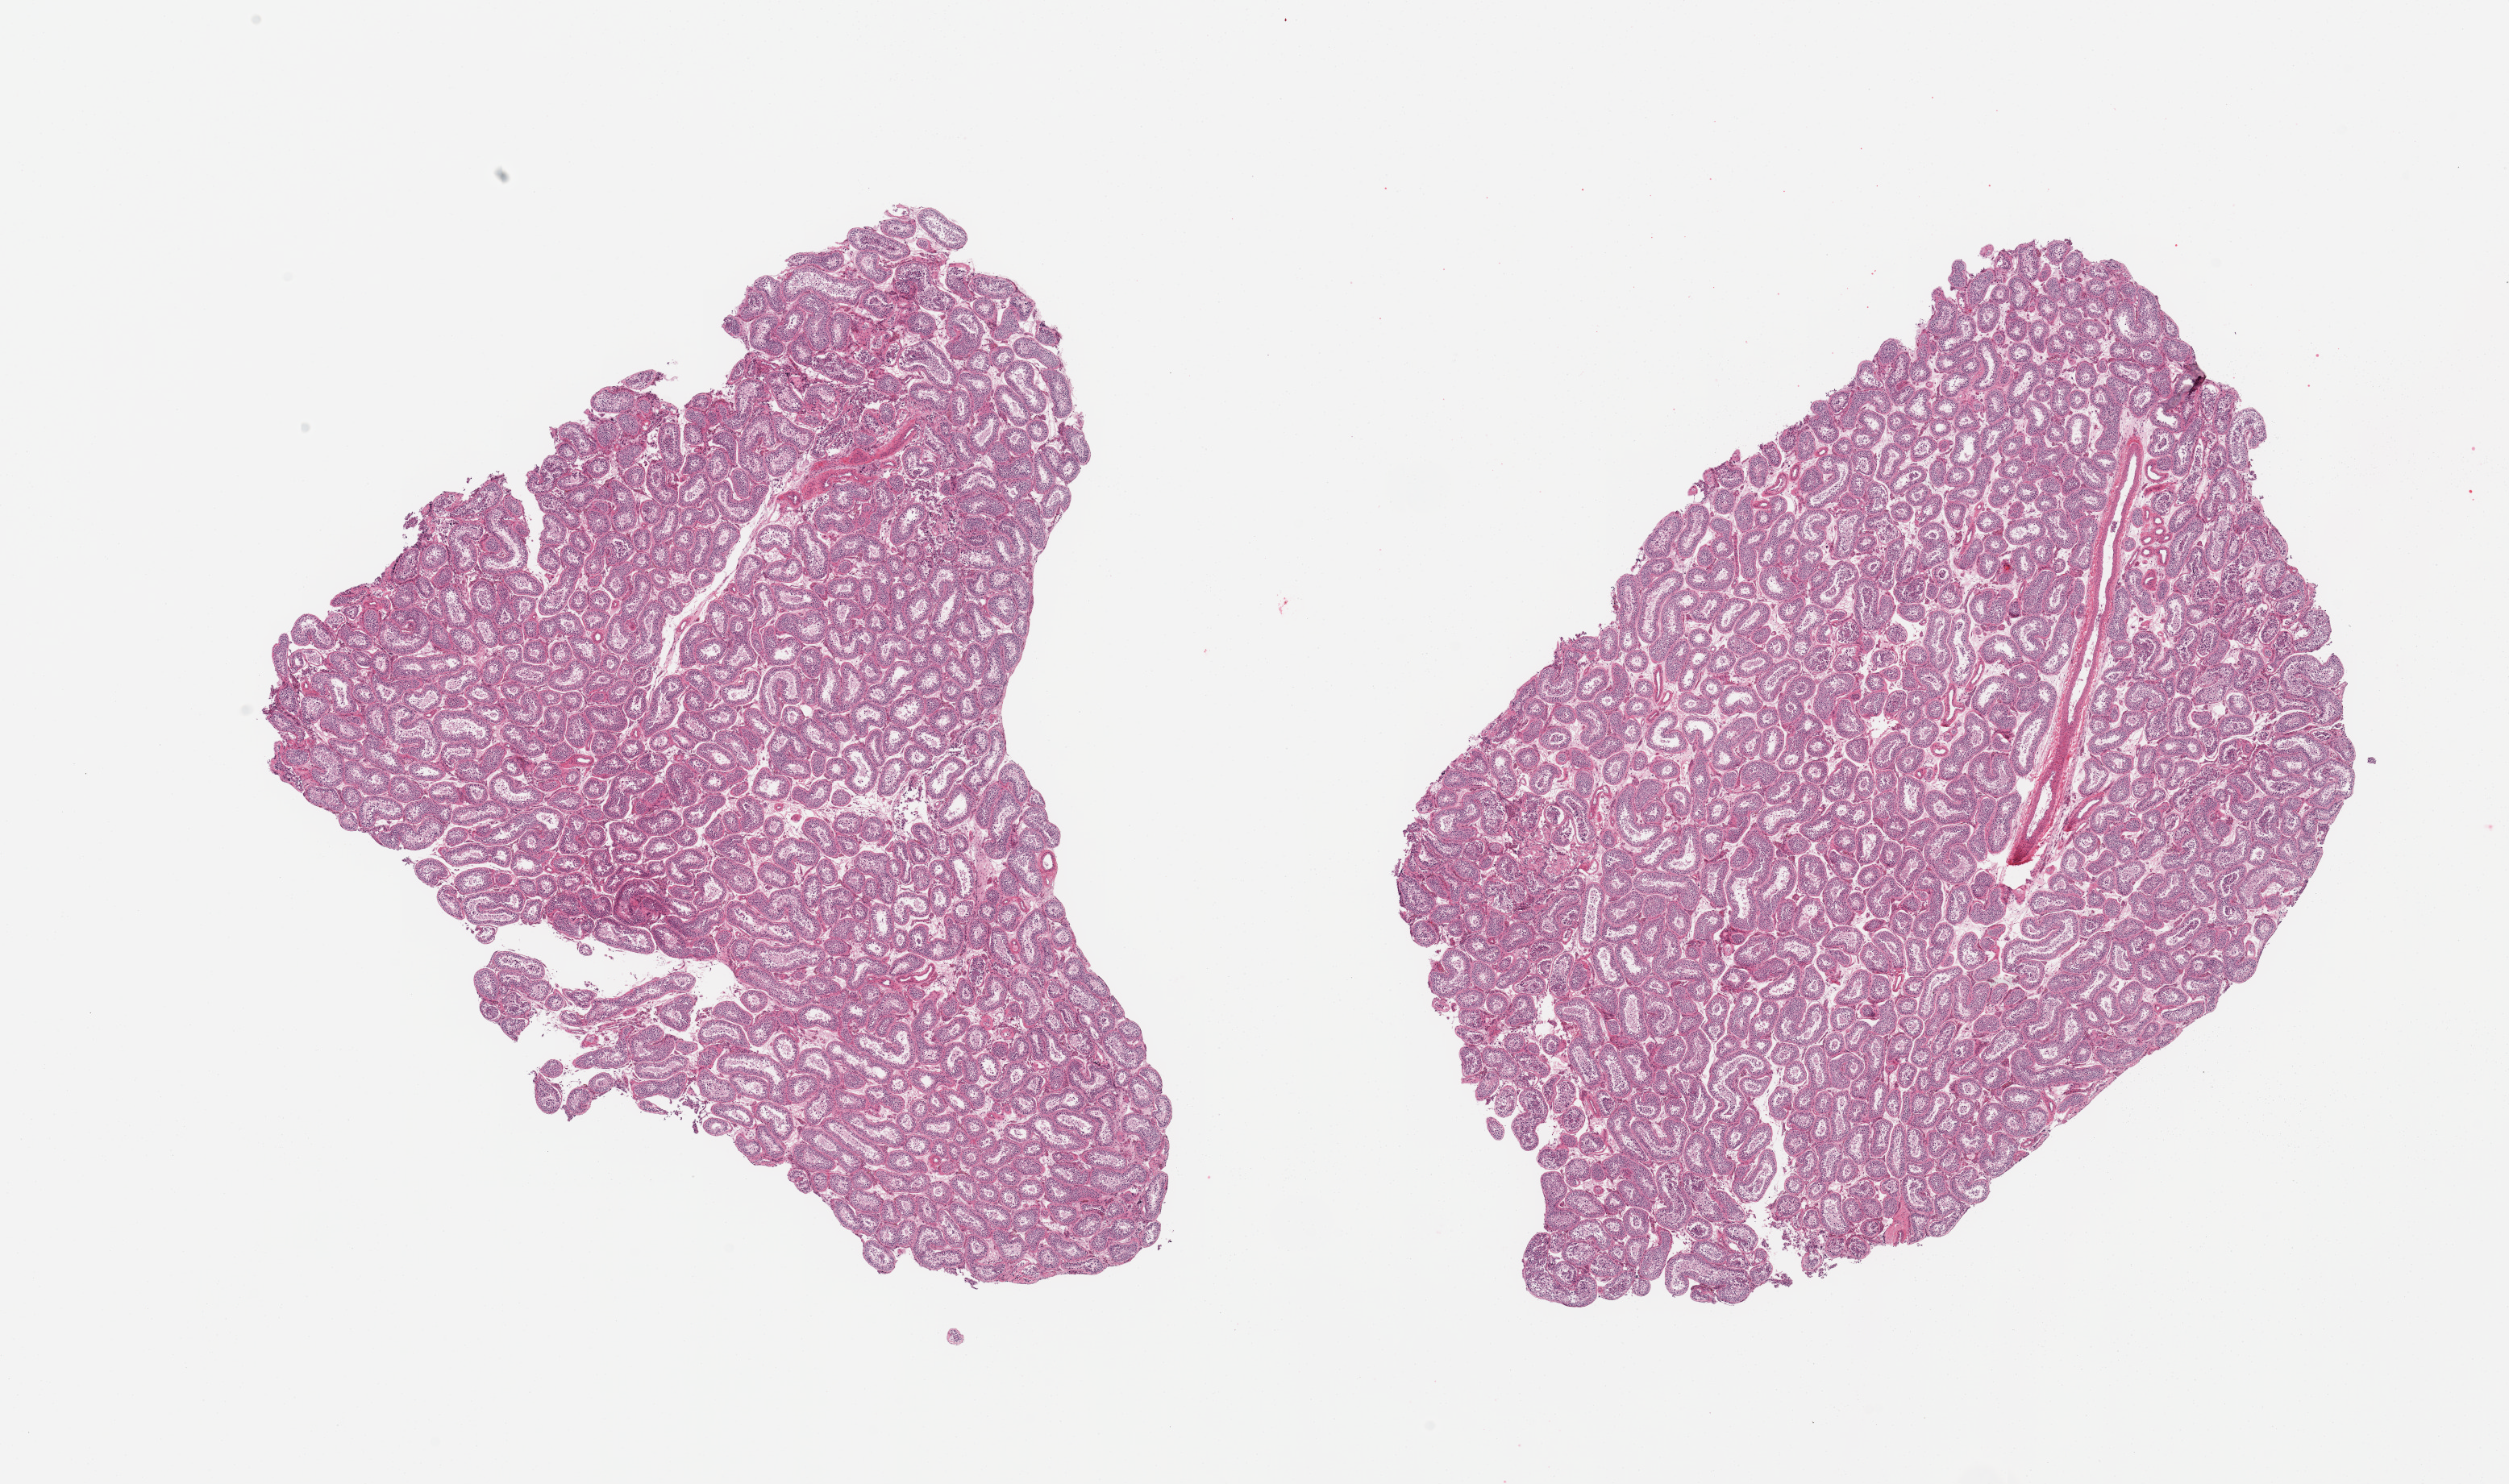
H&E whole-slide image, brightfield, whole scanned area (about 24.6 x 14.6 mm, from a 20x scan) shown as a low-resolution overview, PAXgene-fixed paraffin-embedded (PFPE) section, section of testis (target tissue), tissue donor sample.
Reviewer comment on this tissue sample: 2 pieces; brisk spermatogenesis.